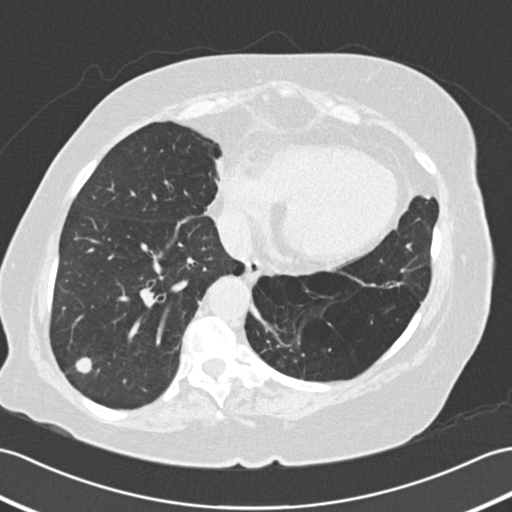
Low-dose screening chest CT, one axial slice; slice 59 of 161 in the series (ordered by position); 120 kVp; lung window (W 1500 / L -600 HU); 2 mm slice thickness; 512 × 512 image matrix, field of view 353 × 353 mm.
Outlined on this slice (outlined manually by an expert reader):
- lesion 1 (tumor, lower lobe of right lung): bounding box <75,357,92,374> (left, top, right, bottom; pixels)